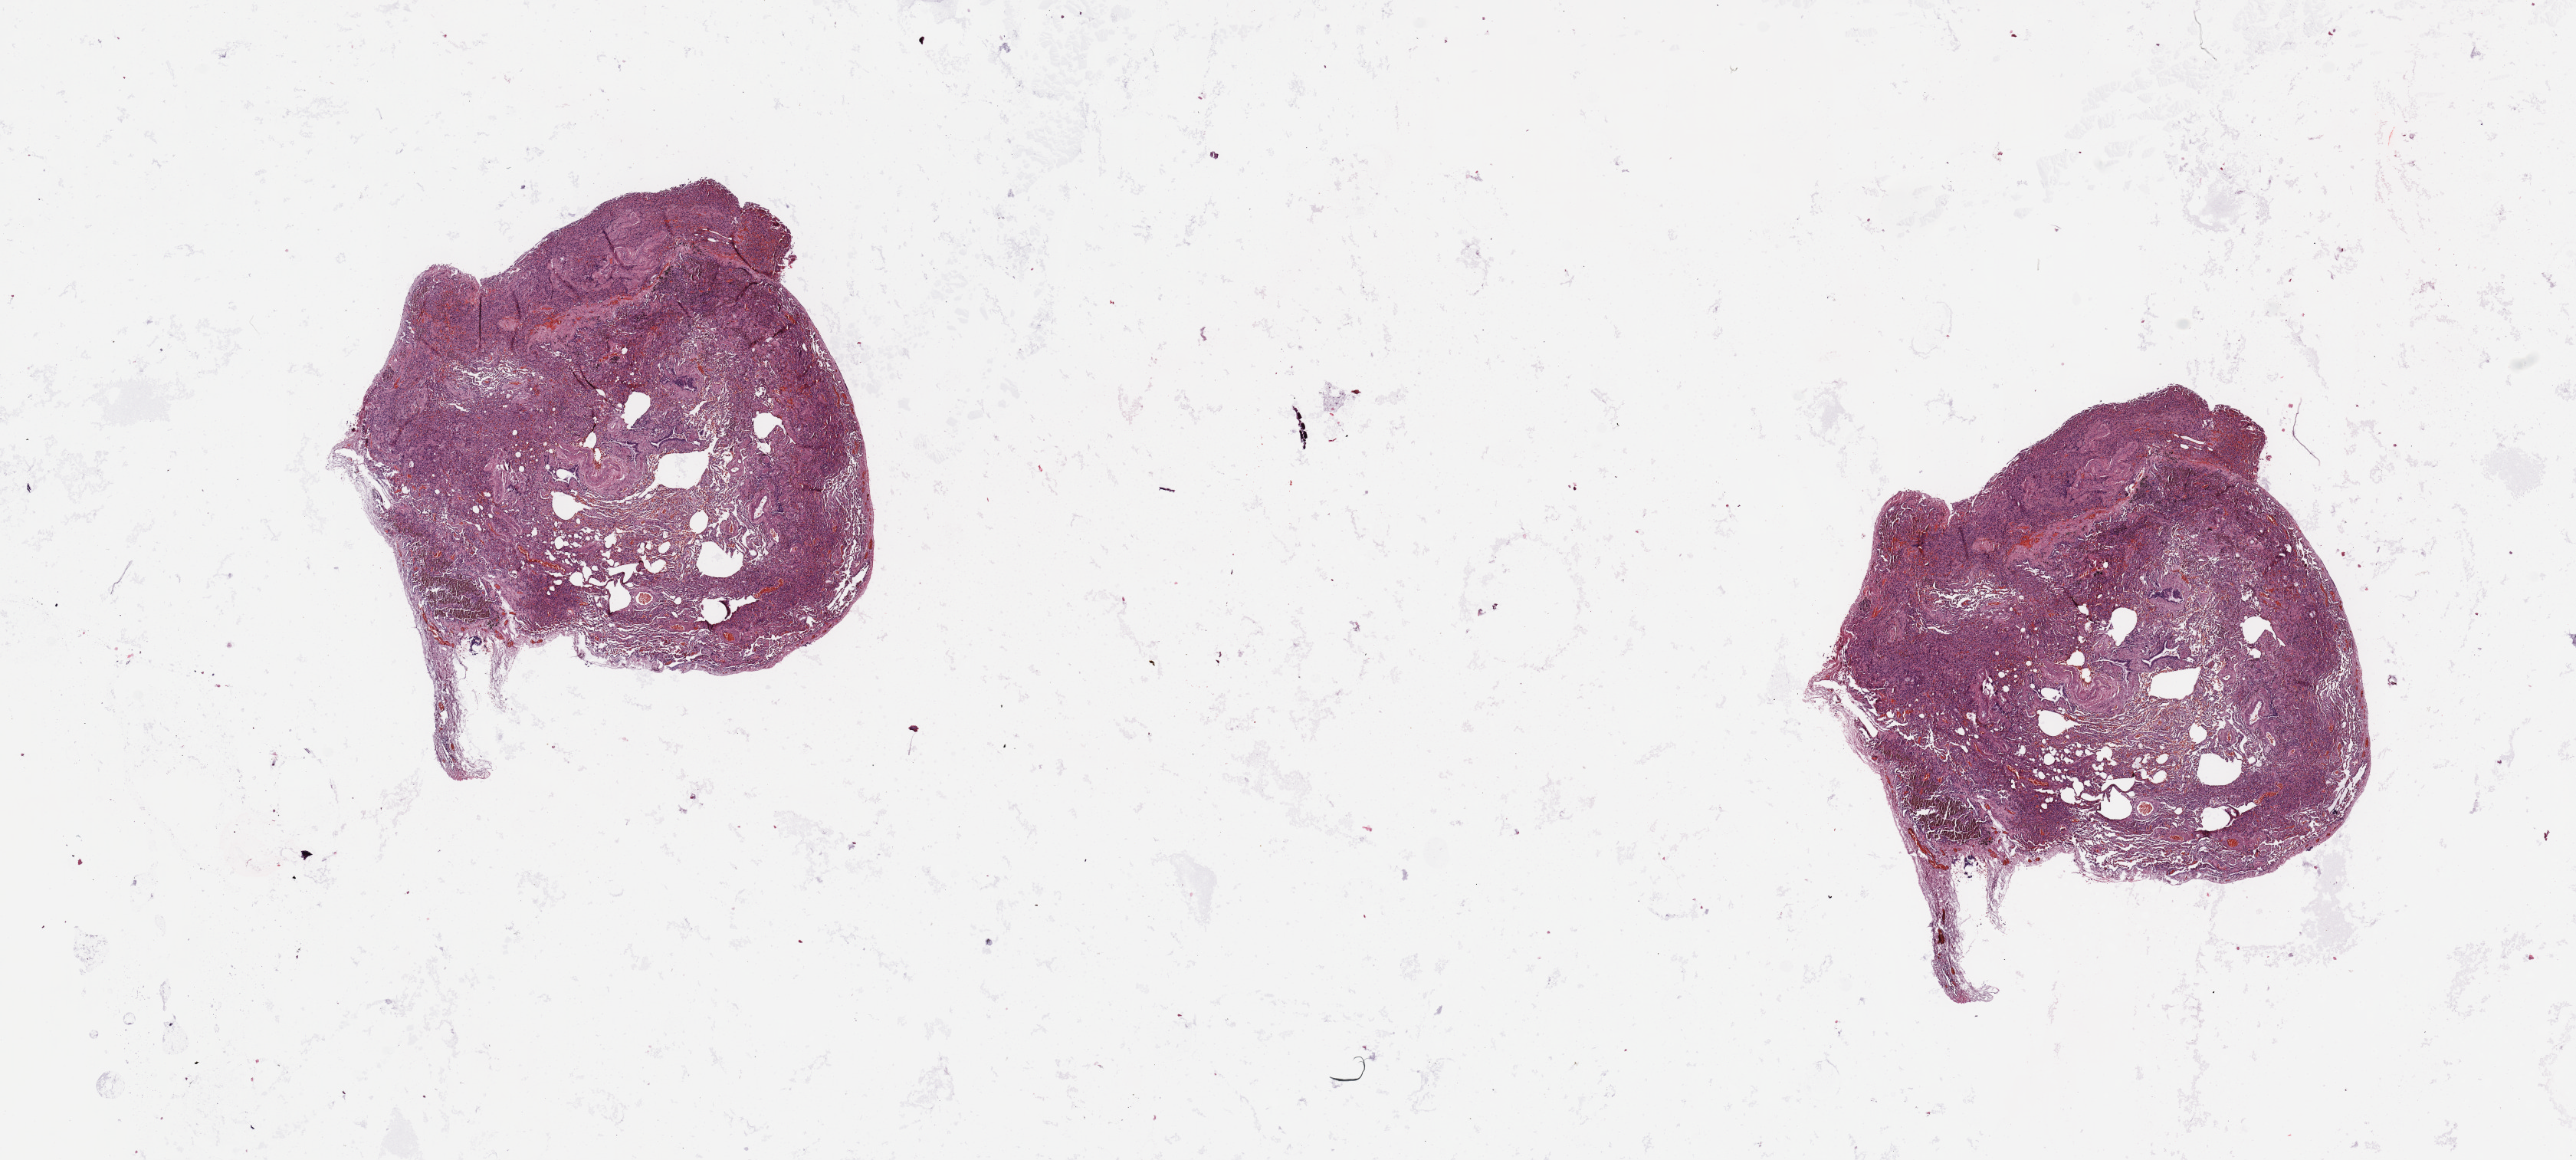
Hematoxylin and eosin (H&E) stained whole-slide image, low-resolution overview of the scanned area, about 26.6 x 12.0 mm; lung, normal (non-tumour) tissue. 63-year-old male patient.
This section: normal (non-tumour) tissue from the same patient. Patient diagnosis (cohort enrolment): squamous cell carcinoma (lung).